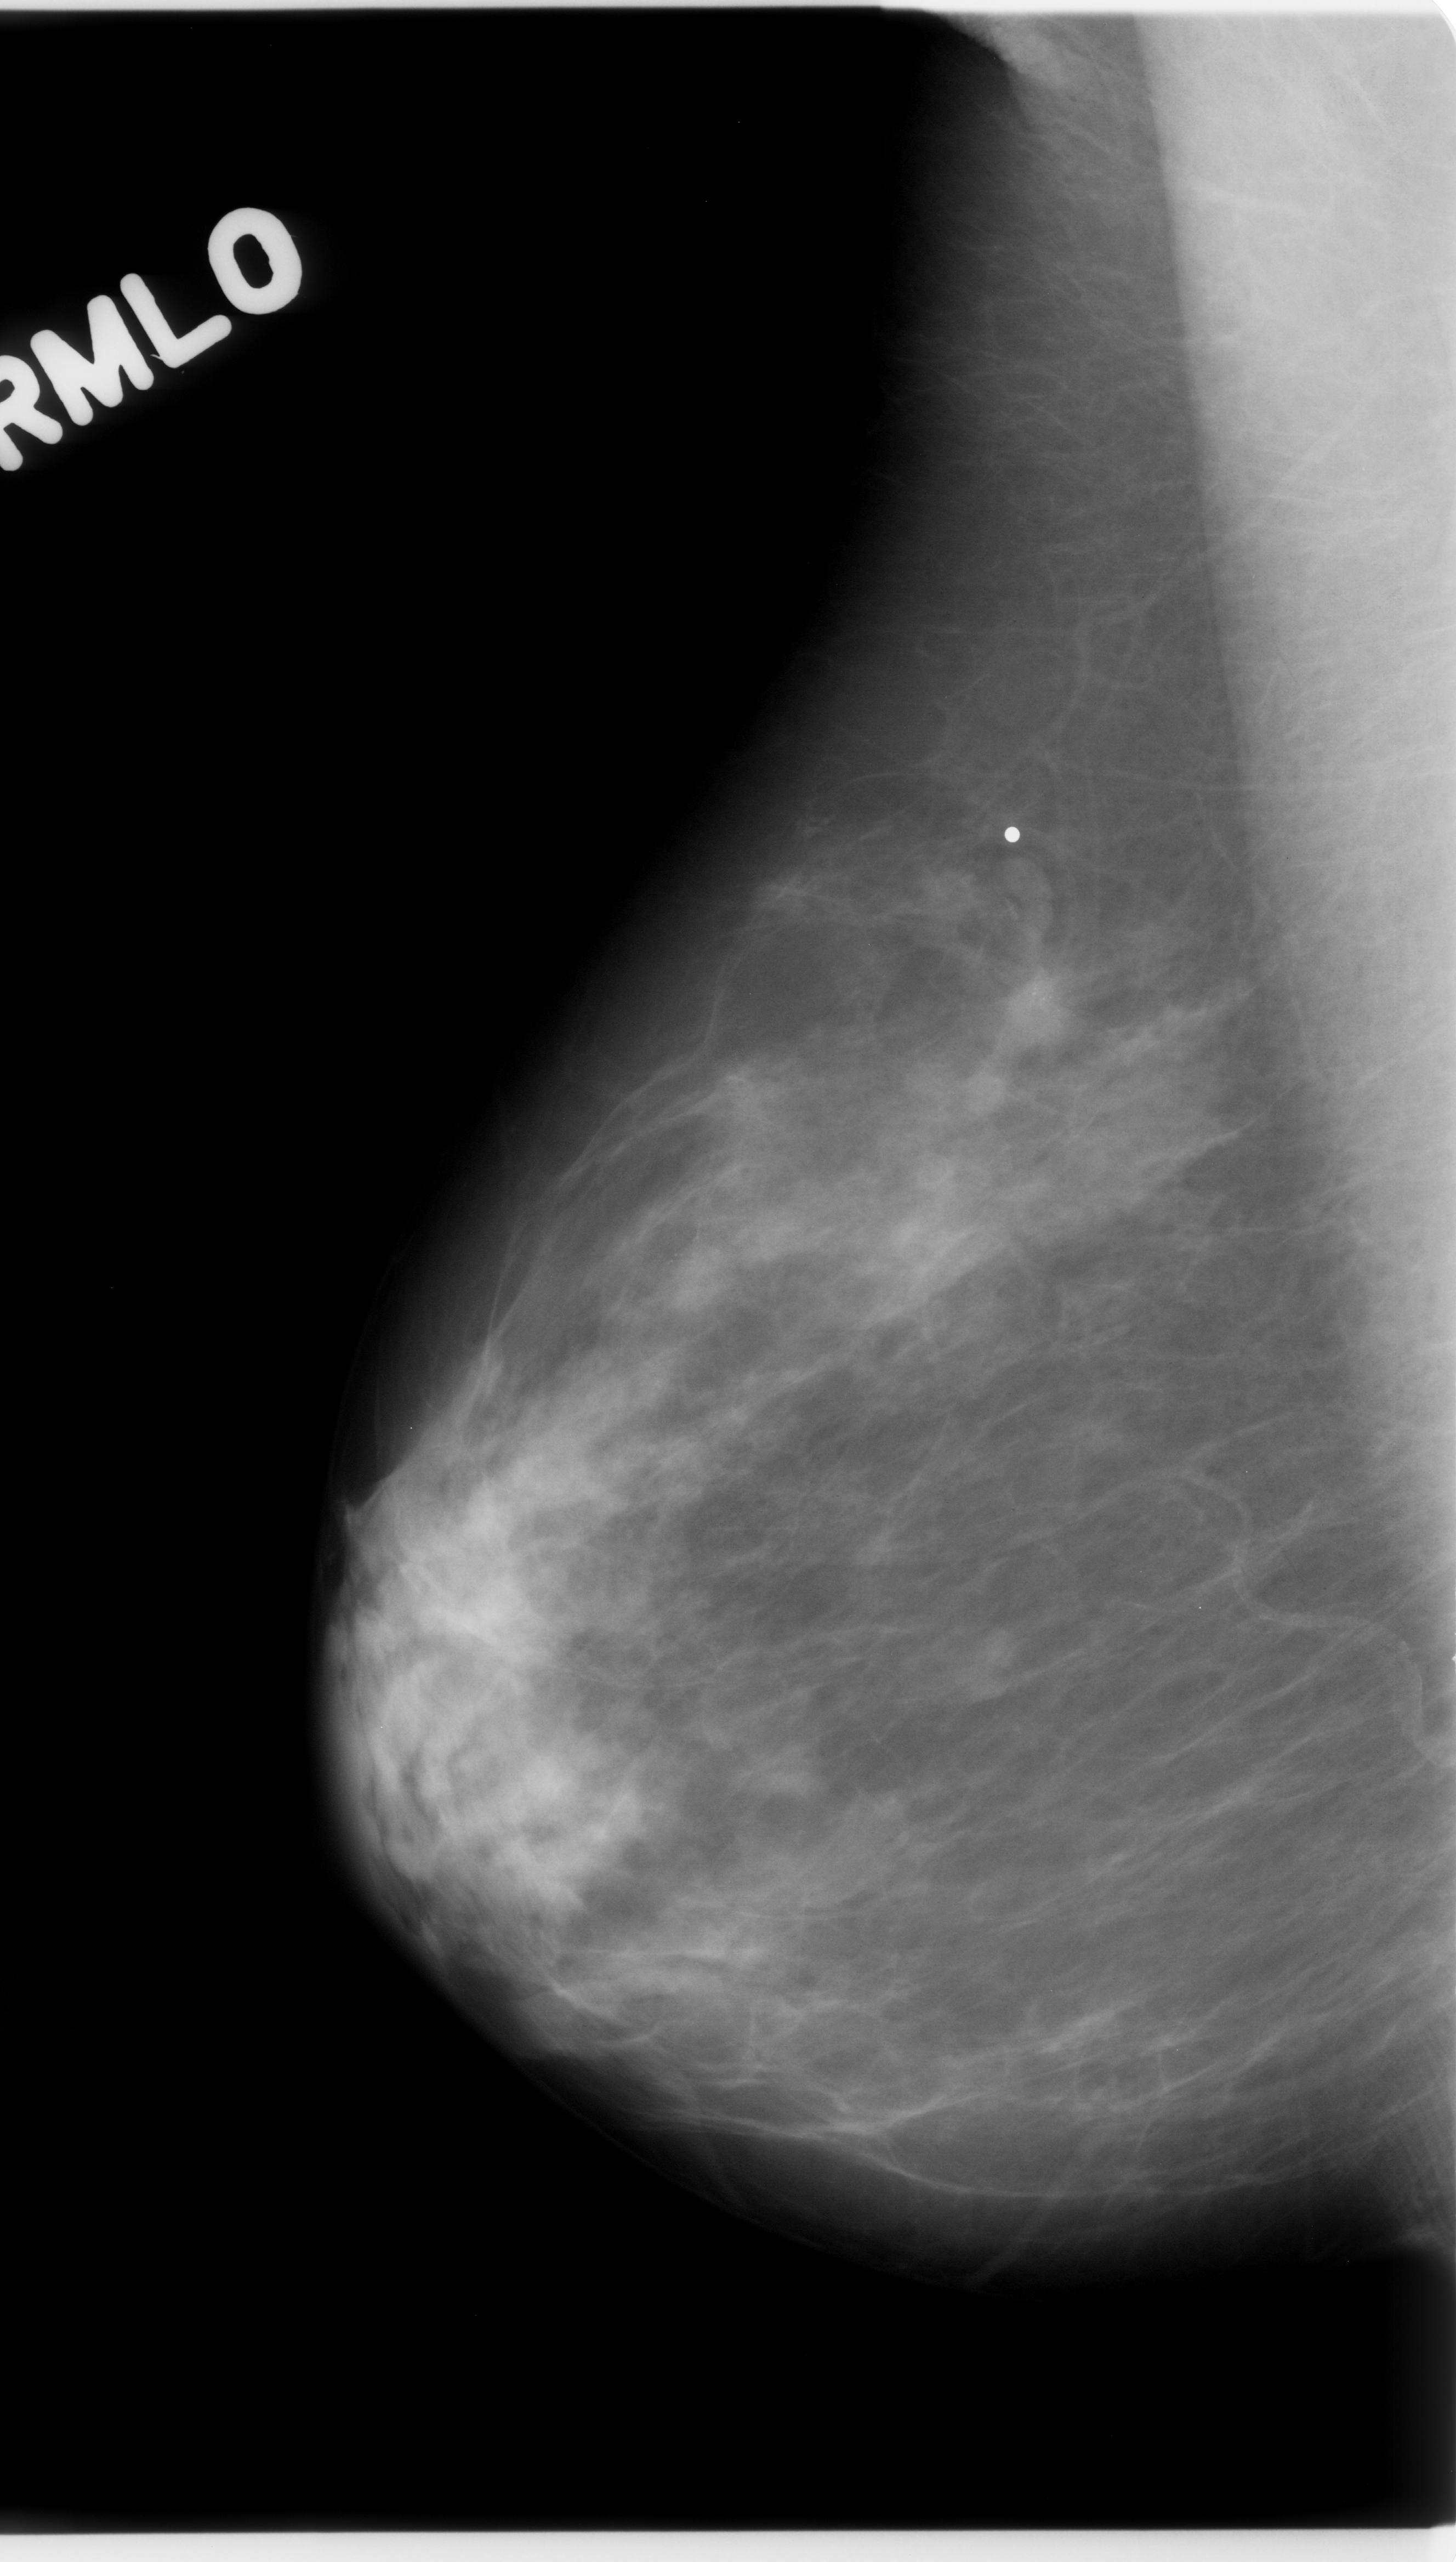
Scanned film-screen mammogram; right breast; MLO view; BI-RADS breast density category 2 (scale 1–4).
- Calcifications, morphology pleomorphic, distribution clustered; BI-RADS assessment category 5; subtlety rating 5 on a 1 (subtle) to 5 (obvious) scale; pathology result (as recorded, not read from the image): malignant.